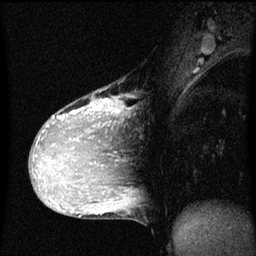
Breast MRI (dynamic contrast-enhanced), one sagittal slice; slice 30 of 60 in the series (ordered by position); dynamic contrast-enhanced series, image 2 of 3 at this slice position (ordered by acquisition); 1.5 T; TE 4.2 ms, TR 8 ms; 2 mm slice thickness; 256 × 256 image matrix, field of view 200 × 200 mm. Patient: female, 36 years.
Annotated regions visible in this slice (semi-automatic segmentation, software-assisted and operator-edited):
- analysis volume of interest (the breast-tissue region the enhancement analysis was run in; not a lesion): box from (x=33, y=90) to (x=119, y=169) px
- tumour enhancement mask (voxels above the 70 % enhancement threshold inside the analysis volume of interest): (x=37, y=100)–(x=119, y=165)